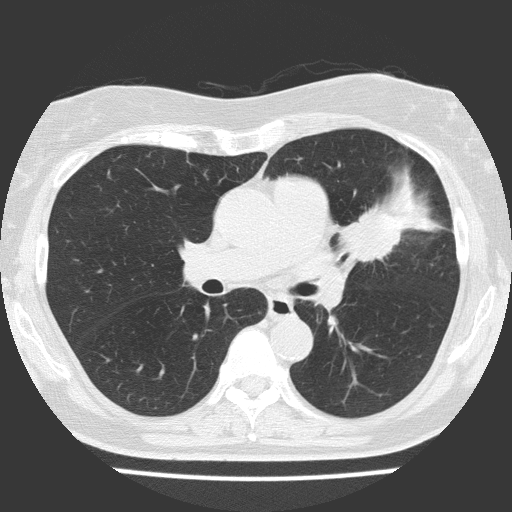
Chest CT (low-dose screening protocol), one axial image, baseline annual screen, lung window (W 1500 / L -600 HU), 2 mm slice thickness, 120 kVp, slice 67 of 151 in the series. Female participant, aged 70 years at enrolment. Current smoker at enrolment.
• Expert-annotated lung lesion, bounding box [x1, y1, x2, y2] px = [325, 187, 433, 279].
• The screening reader recorded 2 non-calcified nodules or masses ≥4 mm on this exam (left upper lobe, right upper lobe); which of them this box marks is not recorded.